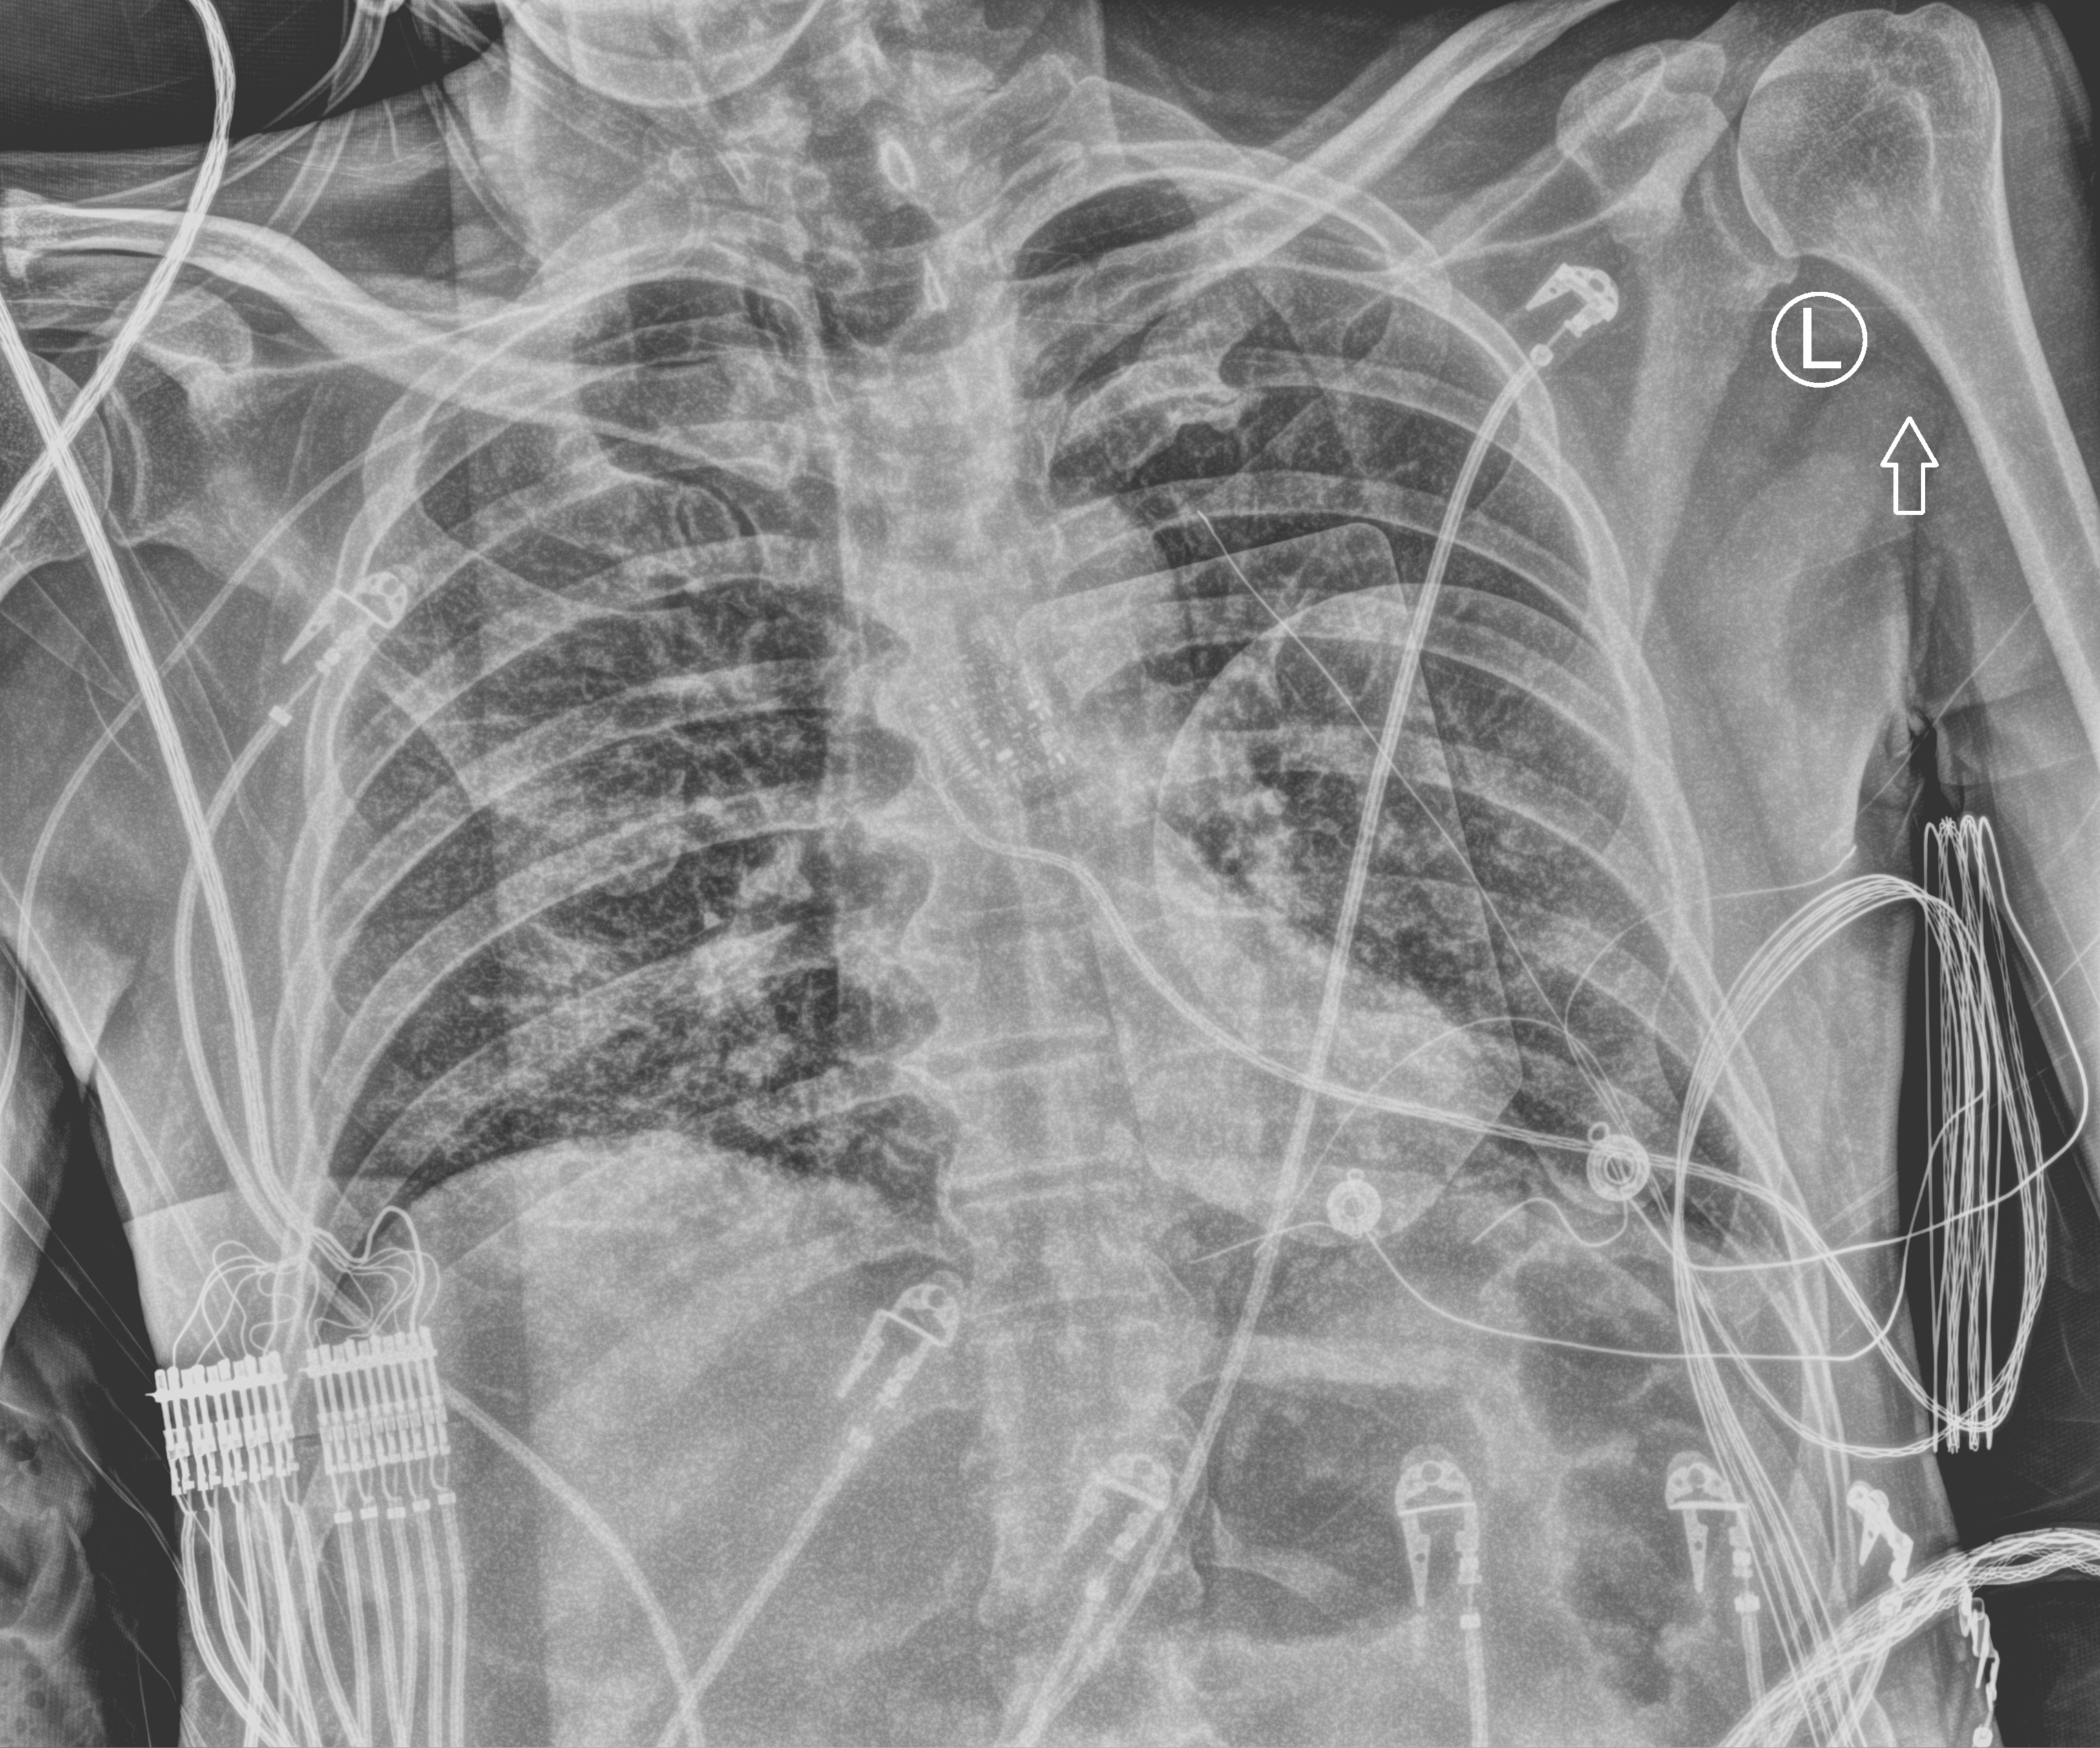
Portable chest radiograph. Patient hospitalised with COVID-19; male, aged 60–74 years.
Admission-level facts for this patient (not findings on this image; timing relative to this image not recorded): chronic kidney disease (admission record): no; mechanically ventilated during this hospital stay: no; COPD (admission record): no.